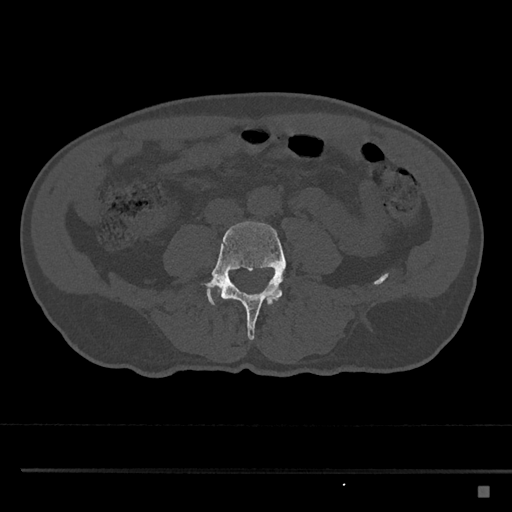
CT including the spine, one axial slice. Slice 635 of 797 in the series (ordered by position). Reconstruction kernel Br40s/3. Bone window (W 1800 / L 400 HU). 0.5 mm slice thickness. 512 × 512 image matrix, field of view 391 × 391 mm. Male patient, age 59 years. From the clinical record (not read from this slice): primary cancer: prostate.
Structures marked on this image (semi-automatically segmented with operator editing):
- L3 vertebra: bounding box (x1, y1, x2, y2) in pixels: (225, 297, 281, 300)
- L4 vertebra: (206, 221, 286, 341)
- L5 vertebra: (206, 275, 216, 306)